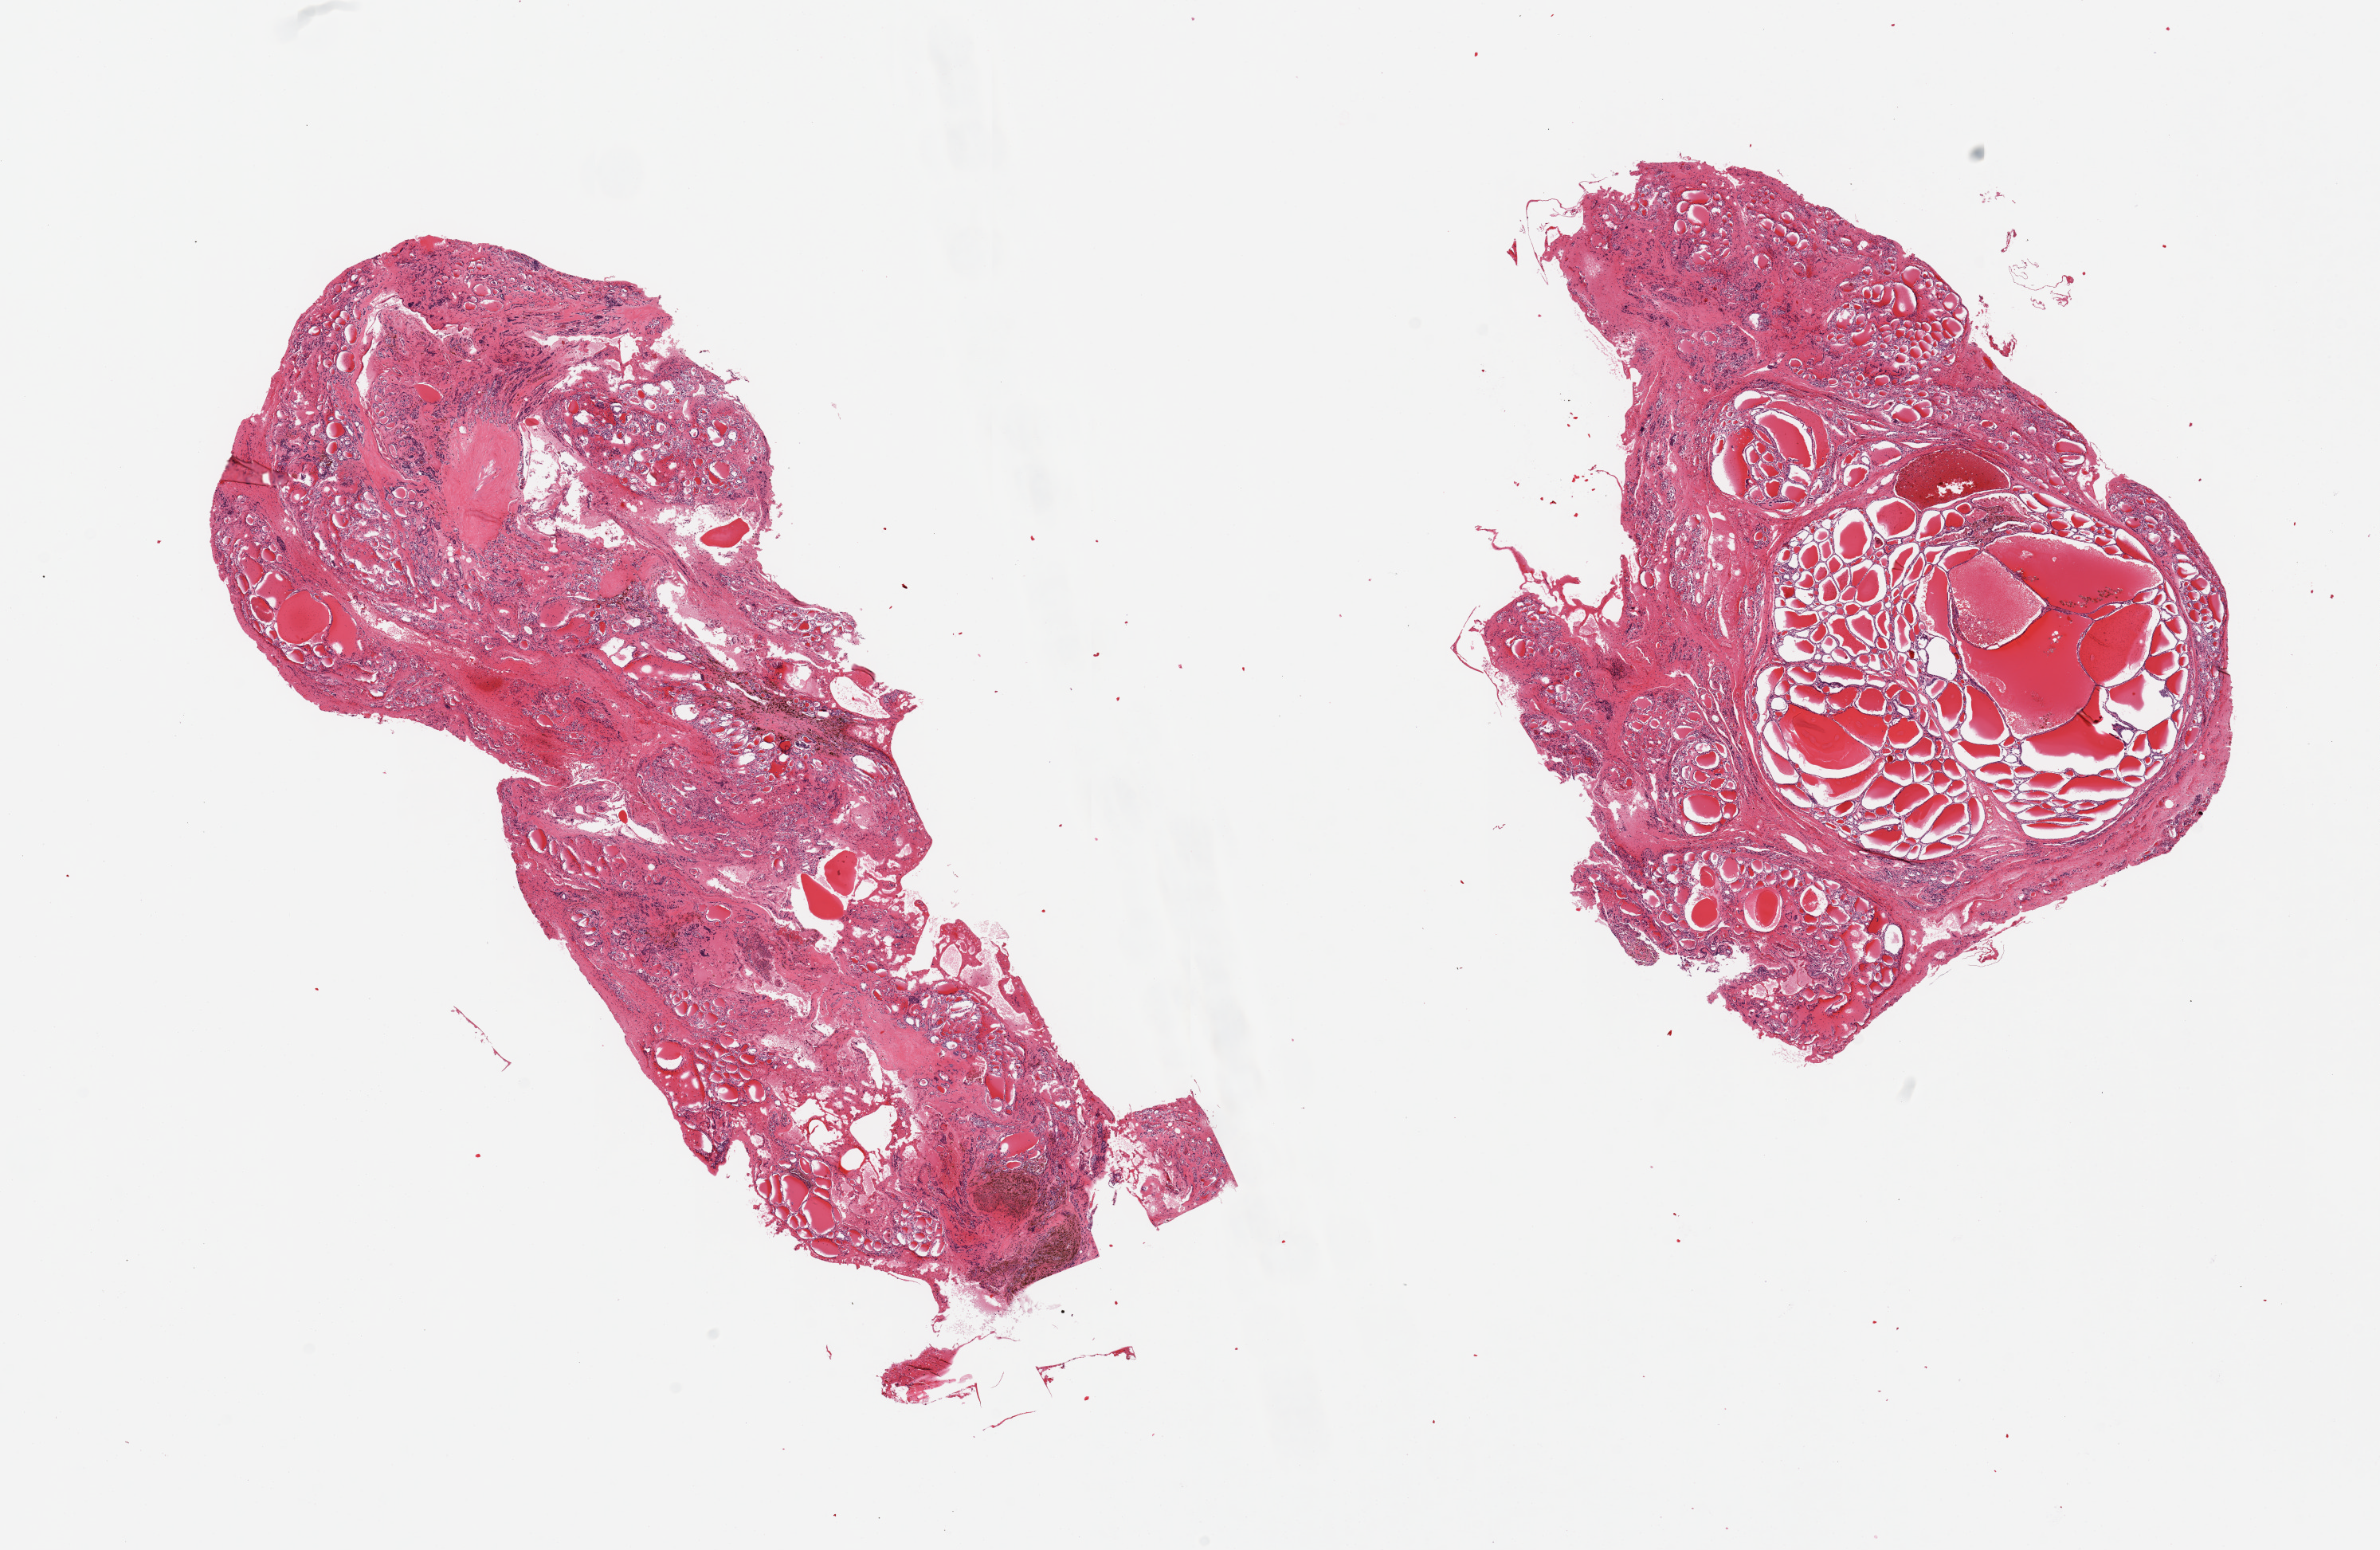
Haematoxylin and eosin whole-slide image, shown as a low-resolution overview of the whole scanned area (about 23.6 x 15.4 mm). PAXgene-fixed, paraffin-embedded tissue. Target tissue: thyroid. Donor tissue sample. Female donor.
Review note (as recorded): 2 pieces; nodular goitre.